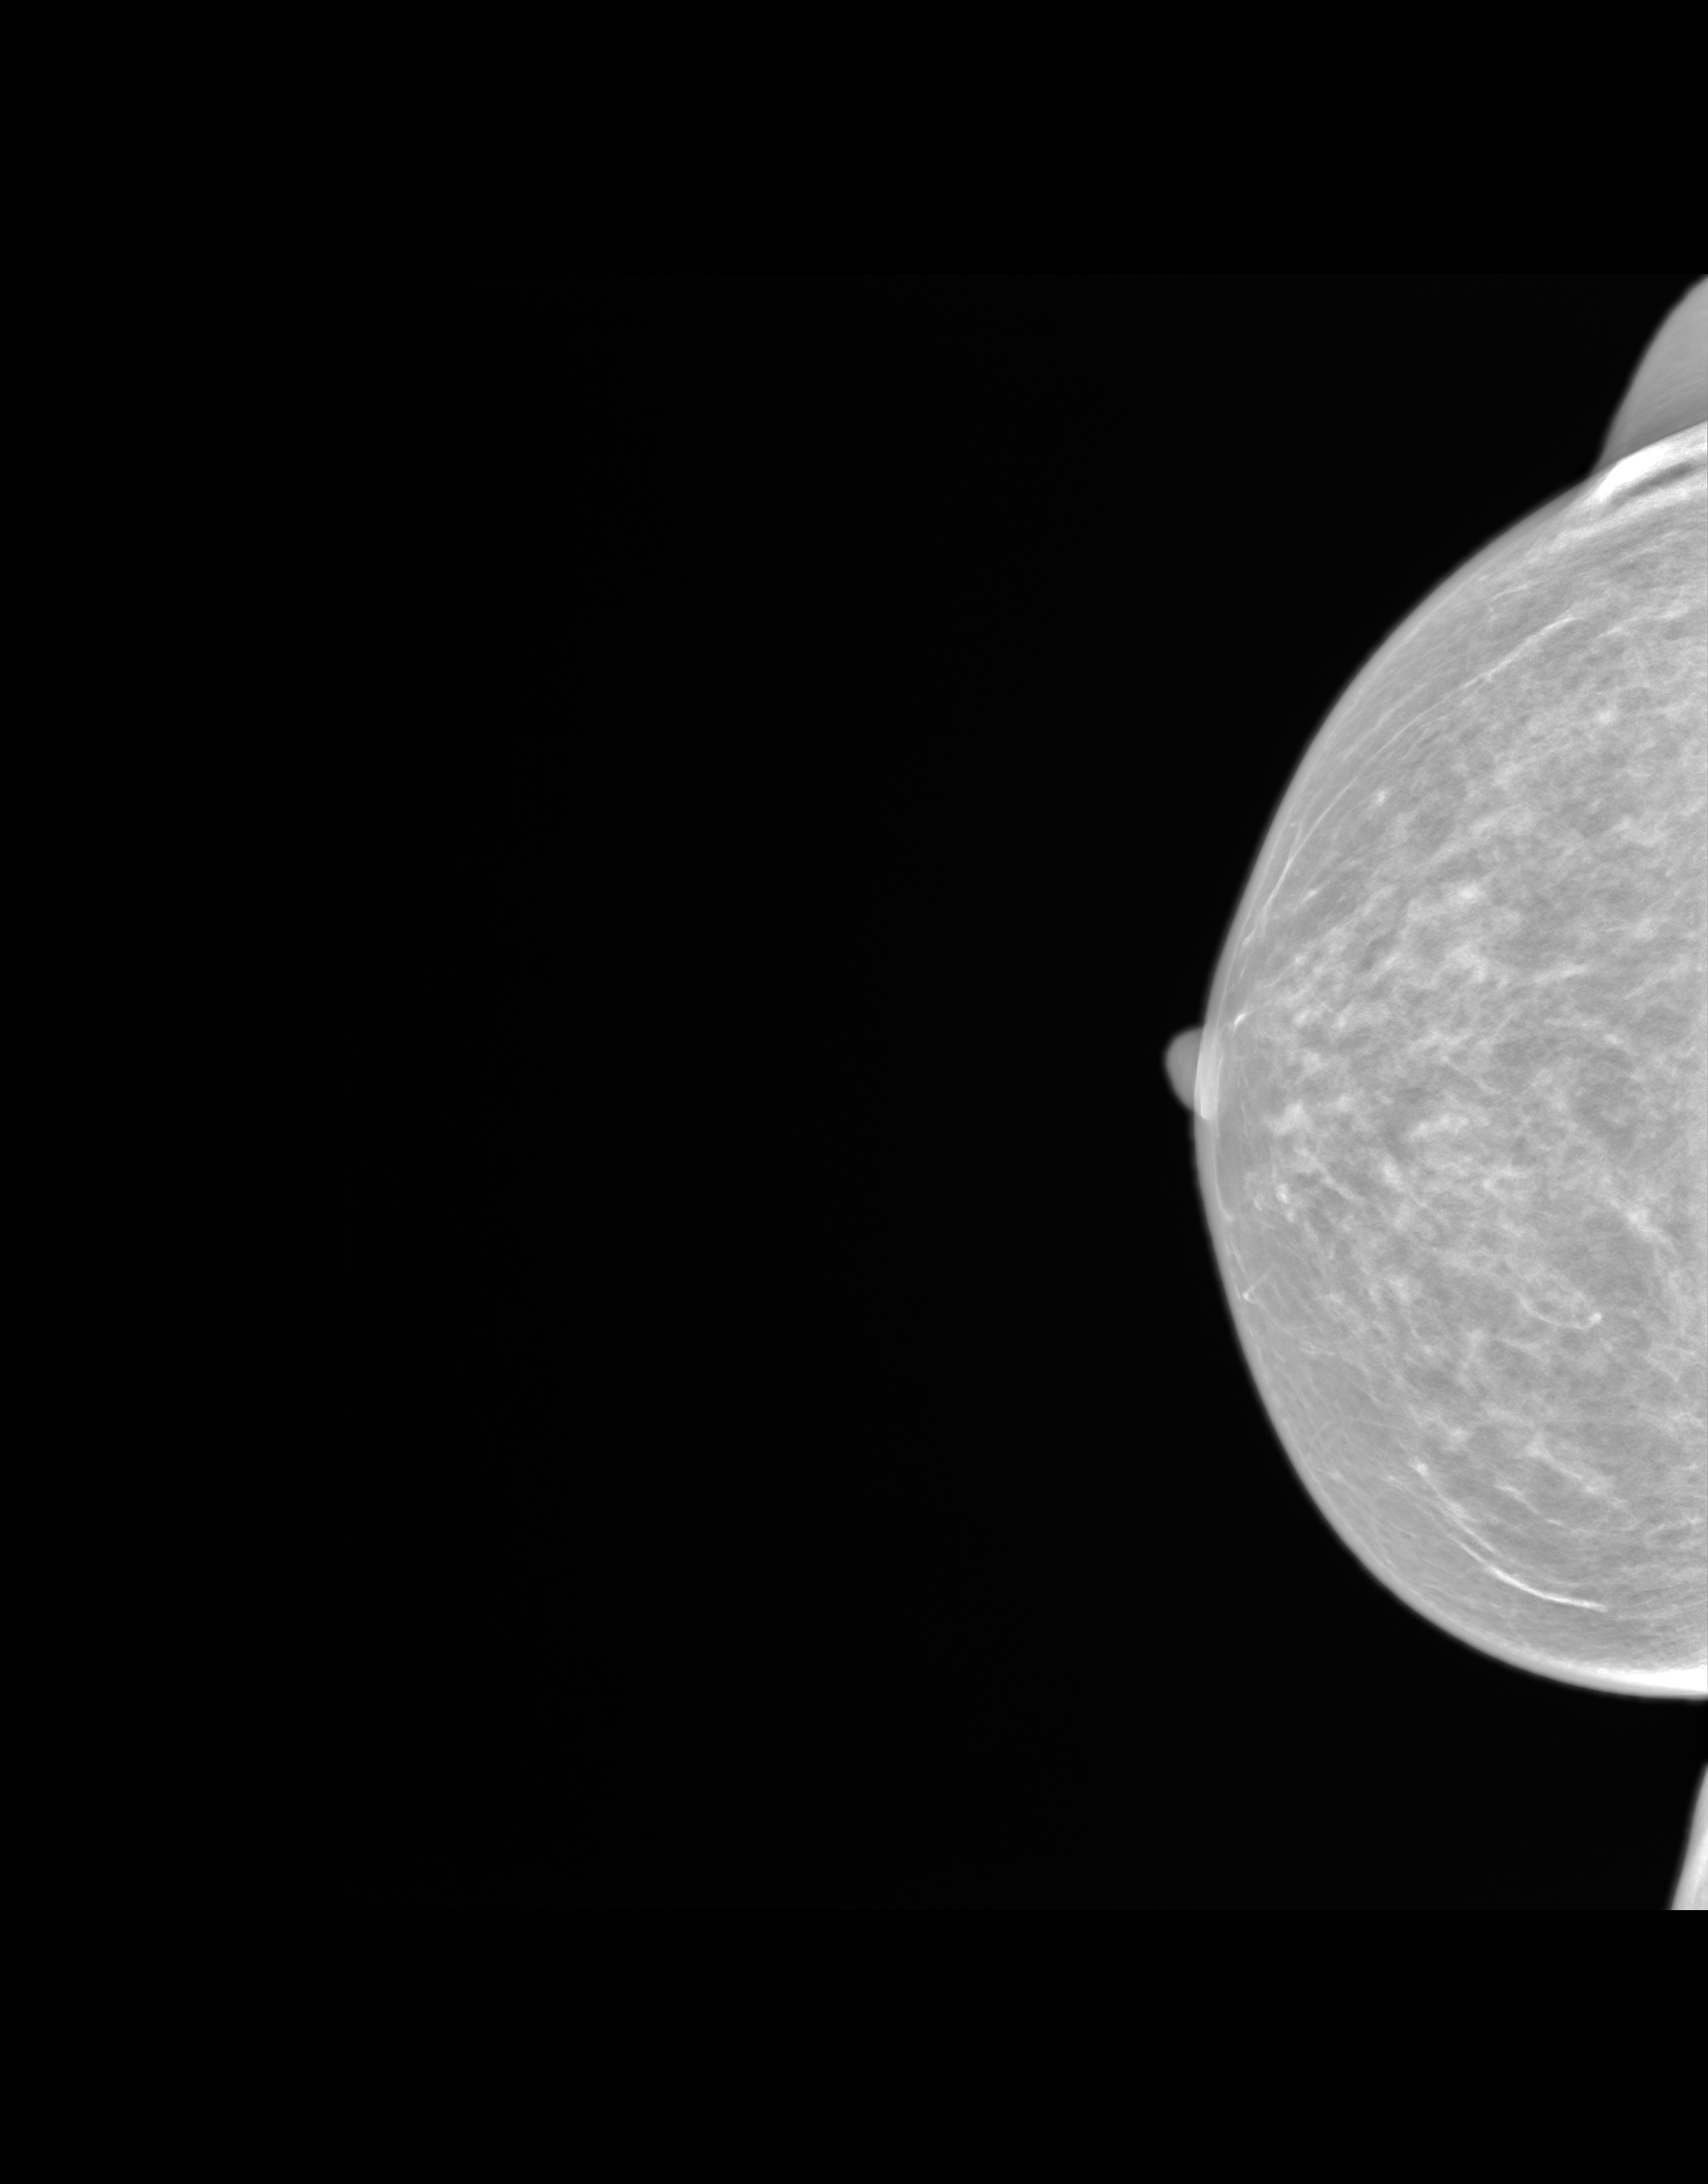
Synthetic 2-D view generated from a tomosynthesis acquisition (not an FFDM exposure); right breast; CC view; annual screening mammography examination; system: SenoIris_1SP1.1(421). Female patient, age 69 years.
Final BI-RADS assessment for this screening round (tomosynthesis exam, both breasts): category 1.